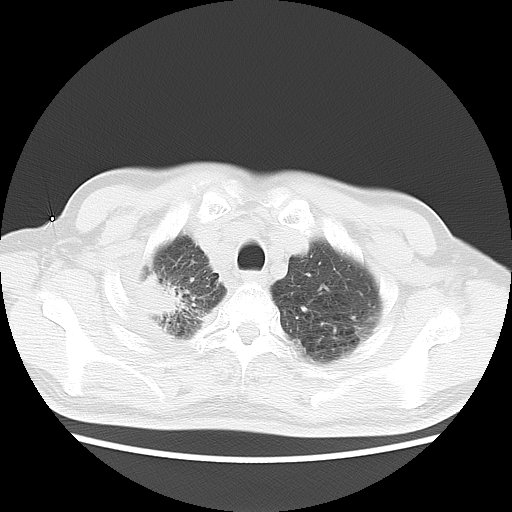
Chest CT, one axial slice. 120 kVp. Lung window (W 1500 / L -600 HU). 5 mm slice thickness. 512 × 512 image matrix. Male patient, age 75 years. Case-level facts recorded for this patient, not image findings: clinical TNM (as recorded): T1c N1 M1.
Structures marked on this image (bounding box drawn by a radiologist):
- lung tumour (recorded histology: adenocarcinoma): bounding box [x1, y1, x2, y2] px = [139, 268, 190, 324]